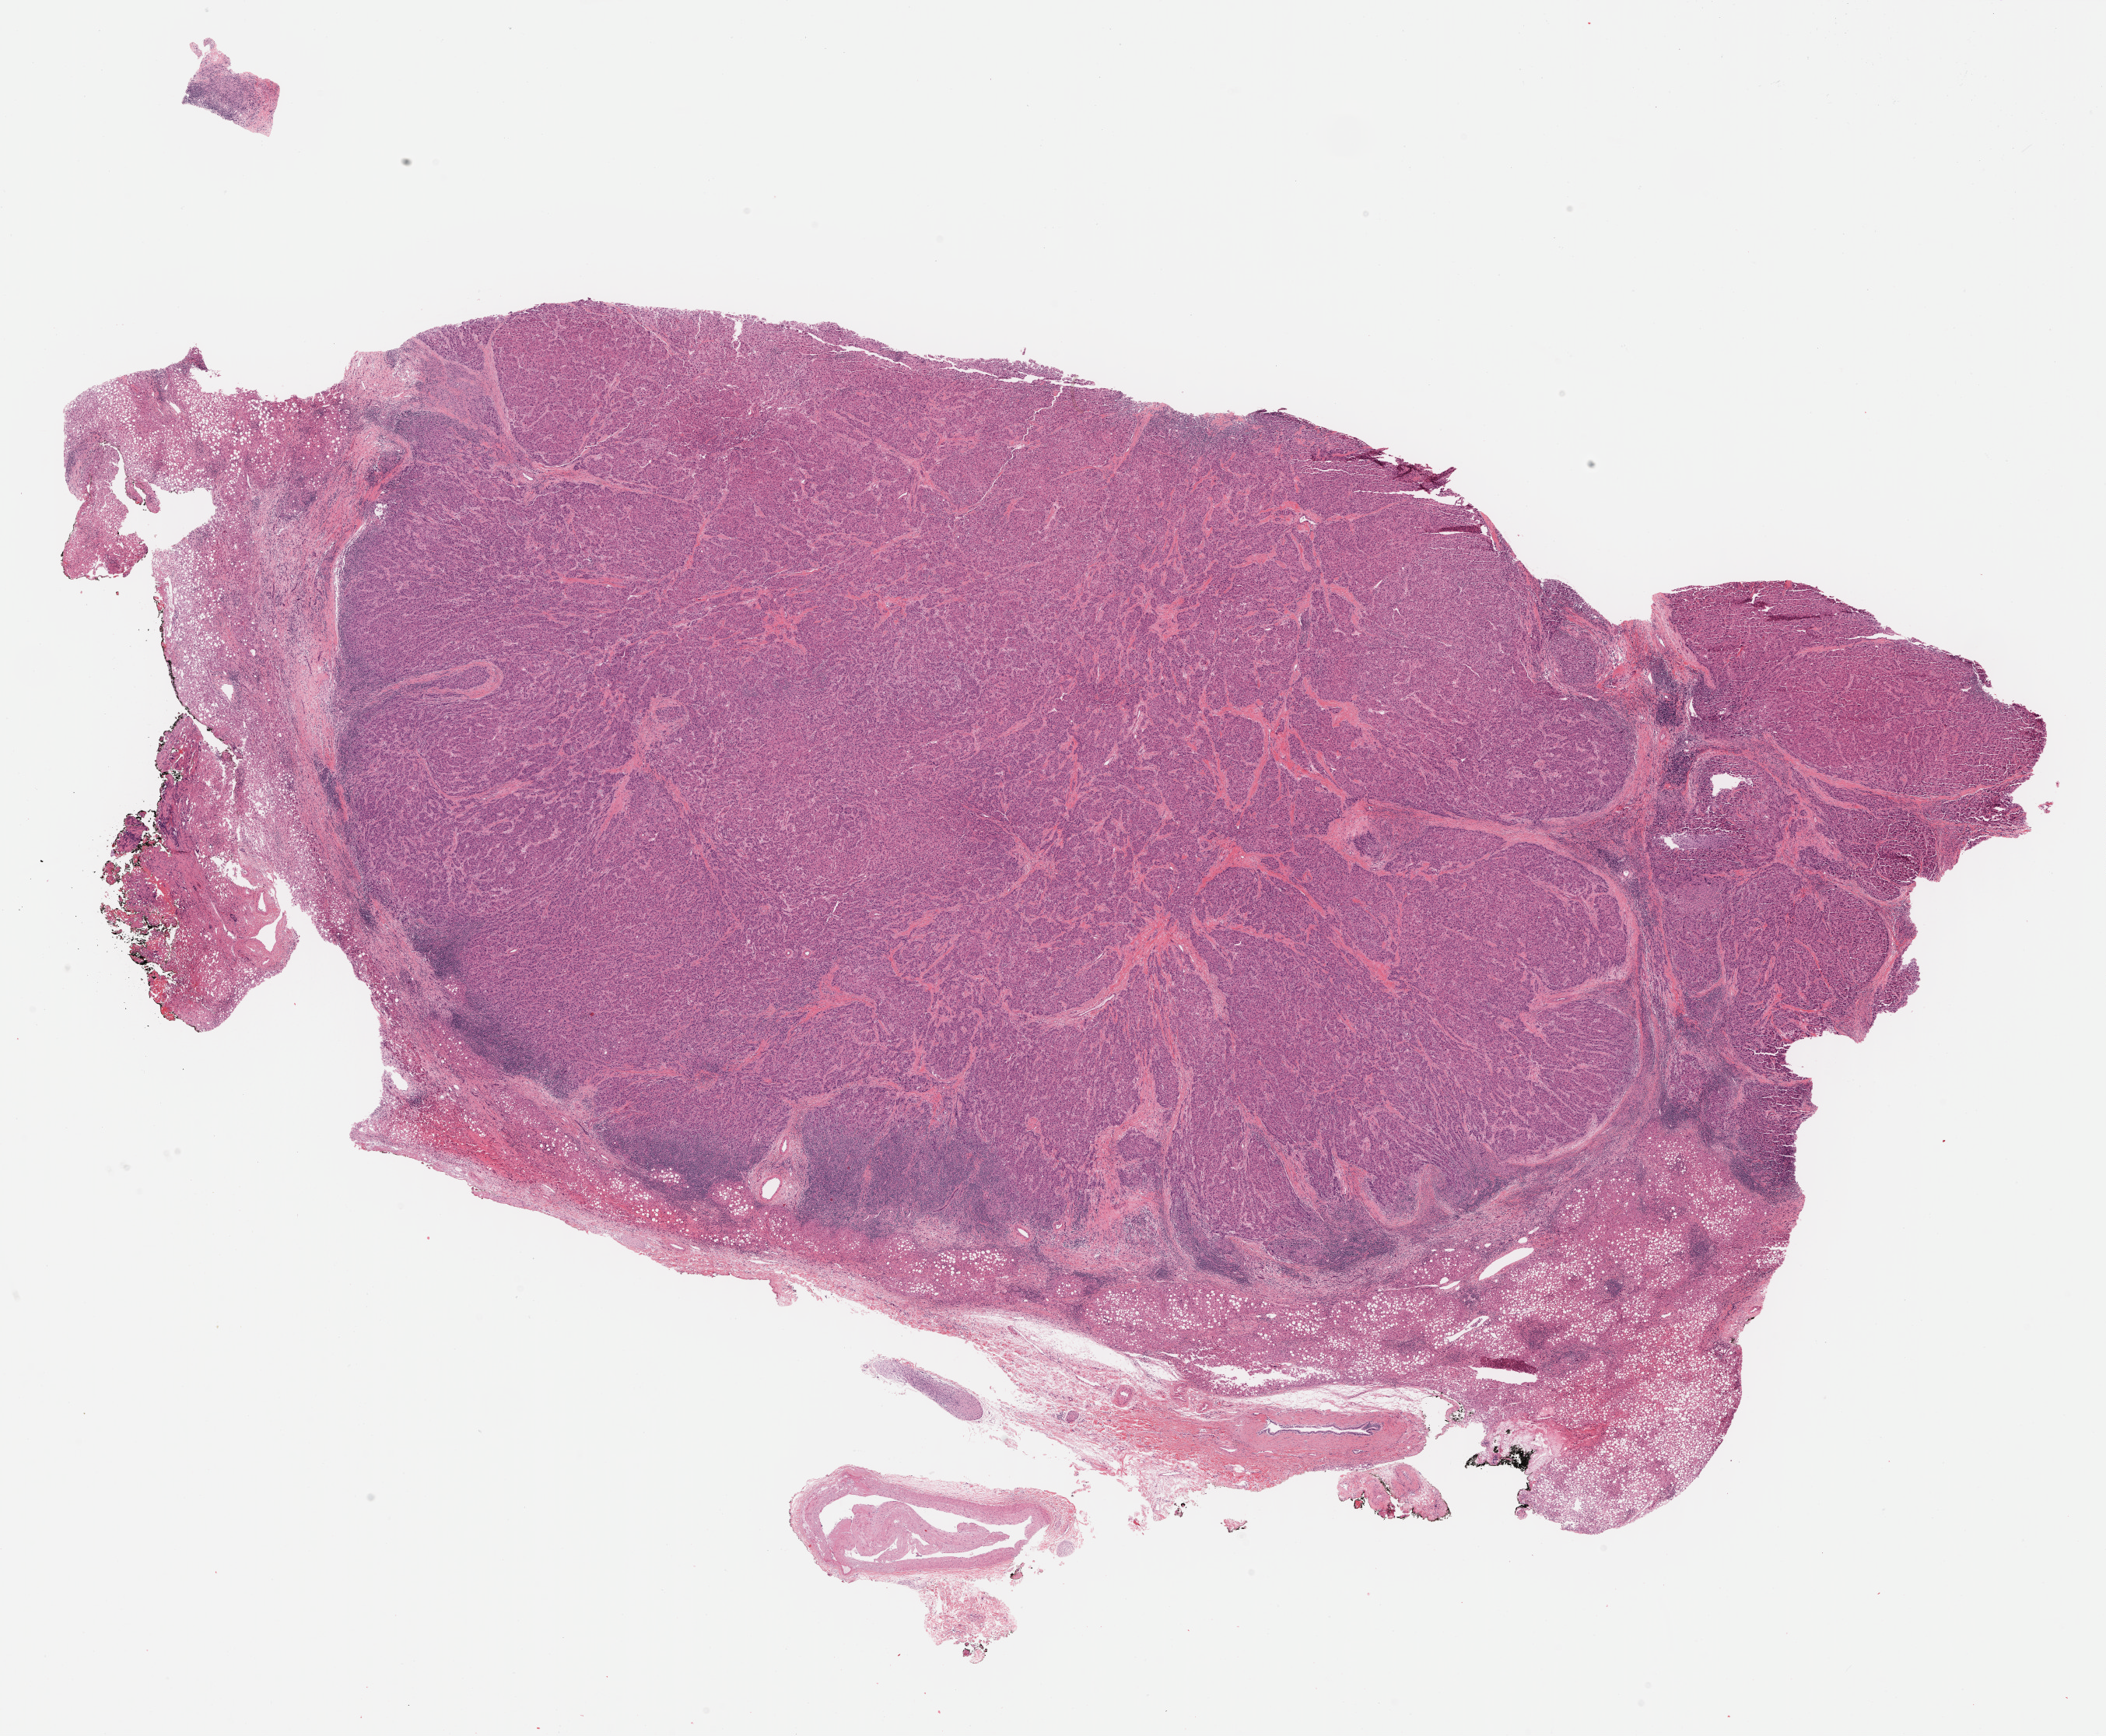
Whole-slide histology image, Hematoxylin and eosin (H&E) stained — shown as a low-resolution overview of the whole scanned area (about 21.9 x 18.1 mm). FFPE section. Liver, primary tumour sample. Male, age 76 years at initial diagnosis. Histologic grade: G3 (poorly differentiated).
AJCC pathologic stage: I (7th edition). Pathologic diagnosis: Hepatocellular carcinoma, NOS.